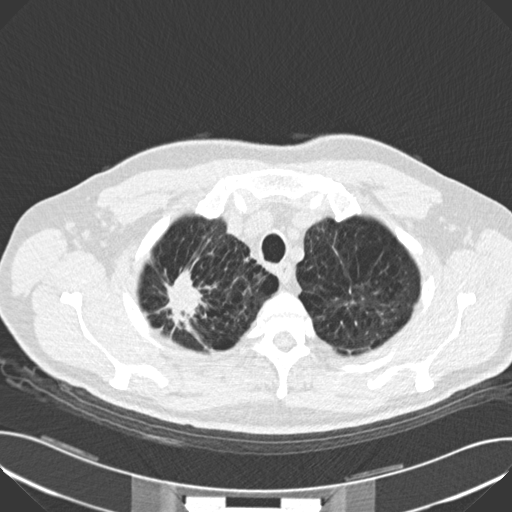
Low-dose screening chest CT, one axial slice. Position 139 of 159 along the scan axis. Reconstruction kernel B30f. Lung window (W 1500 / L -600 HU). 2 mm slice thickness. 512 × 512 image matrix, field of view 380 × 380 mm.
Structures marked on this image (expert manual segmentation):
- lesion 1 (tumor, upper lobe of right lung): box from (x=167, y=269) to (x=203, y=323) px